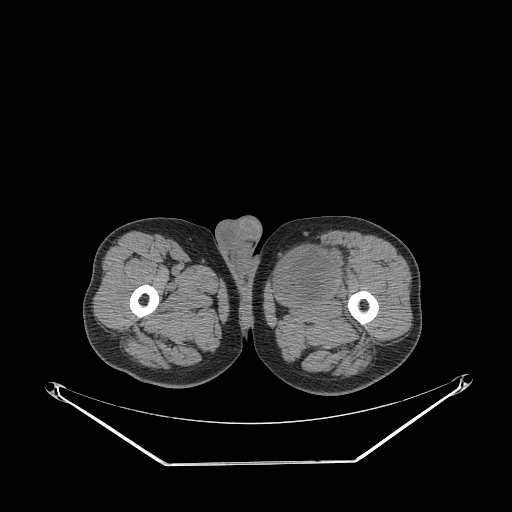
CT of an extremity soft-tissue mass (from a PET/CT study), one axial slice; slice 260 of 267 in the series (ordered by position); reconstruction kernel STANDARD; 140 kVp; soft-tissue window (W 400 / L 40 HU); 3.75 mm slice thickness; 512 × 512 image matrix, field of view 500 × 500 mm. Male patient. Case-level facts recorded for this patient, not image findings: histological type: pleiomorphic liposarcoma; grade: high; site of the primary tumour: left thigh.
Structures marked on this image (expert contour drawn on MRI and transferred to this co-registered scan by the dataset authors):
- gross tumour volume including surrounding oedema: box from (x=279, y=242) to (x=346, y=296) px
- gross tumour volume (mass): (x=279, y=249)–(x=334, y=295)